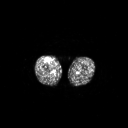
FDG PET of an extremity soft-tissue mass (from a PET/CT study), one axial slice. Slice 237 of 311 in the series (ordered by position). 3.27 mm slice thickness. 128 × 128 image matrix, field of view 700 × 700 mm. Patient: male, 56 years. From the clinical record (not read from this slice): histological type: pleiomorphic leiomyosarcoma; grade: intermediate; site of the primary tumour: right thigh.
Annotated regions visible in this slice (expert contour drawn on MRI and transferred to this co-registered scan by the dataset authors):
- gross tumour volume including surrounding oedema: bounding box (x1, y1, x2, y2) in pixels: (45, 58, 51, 62)